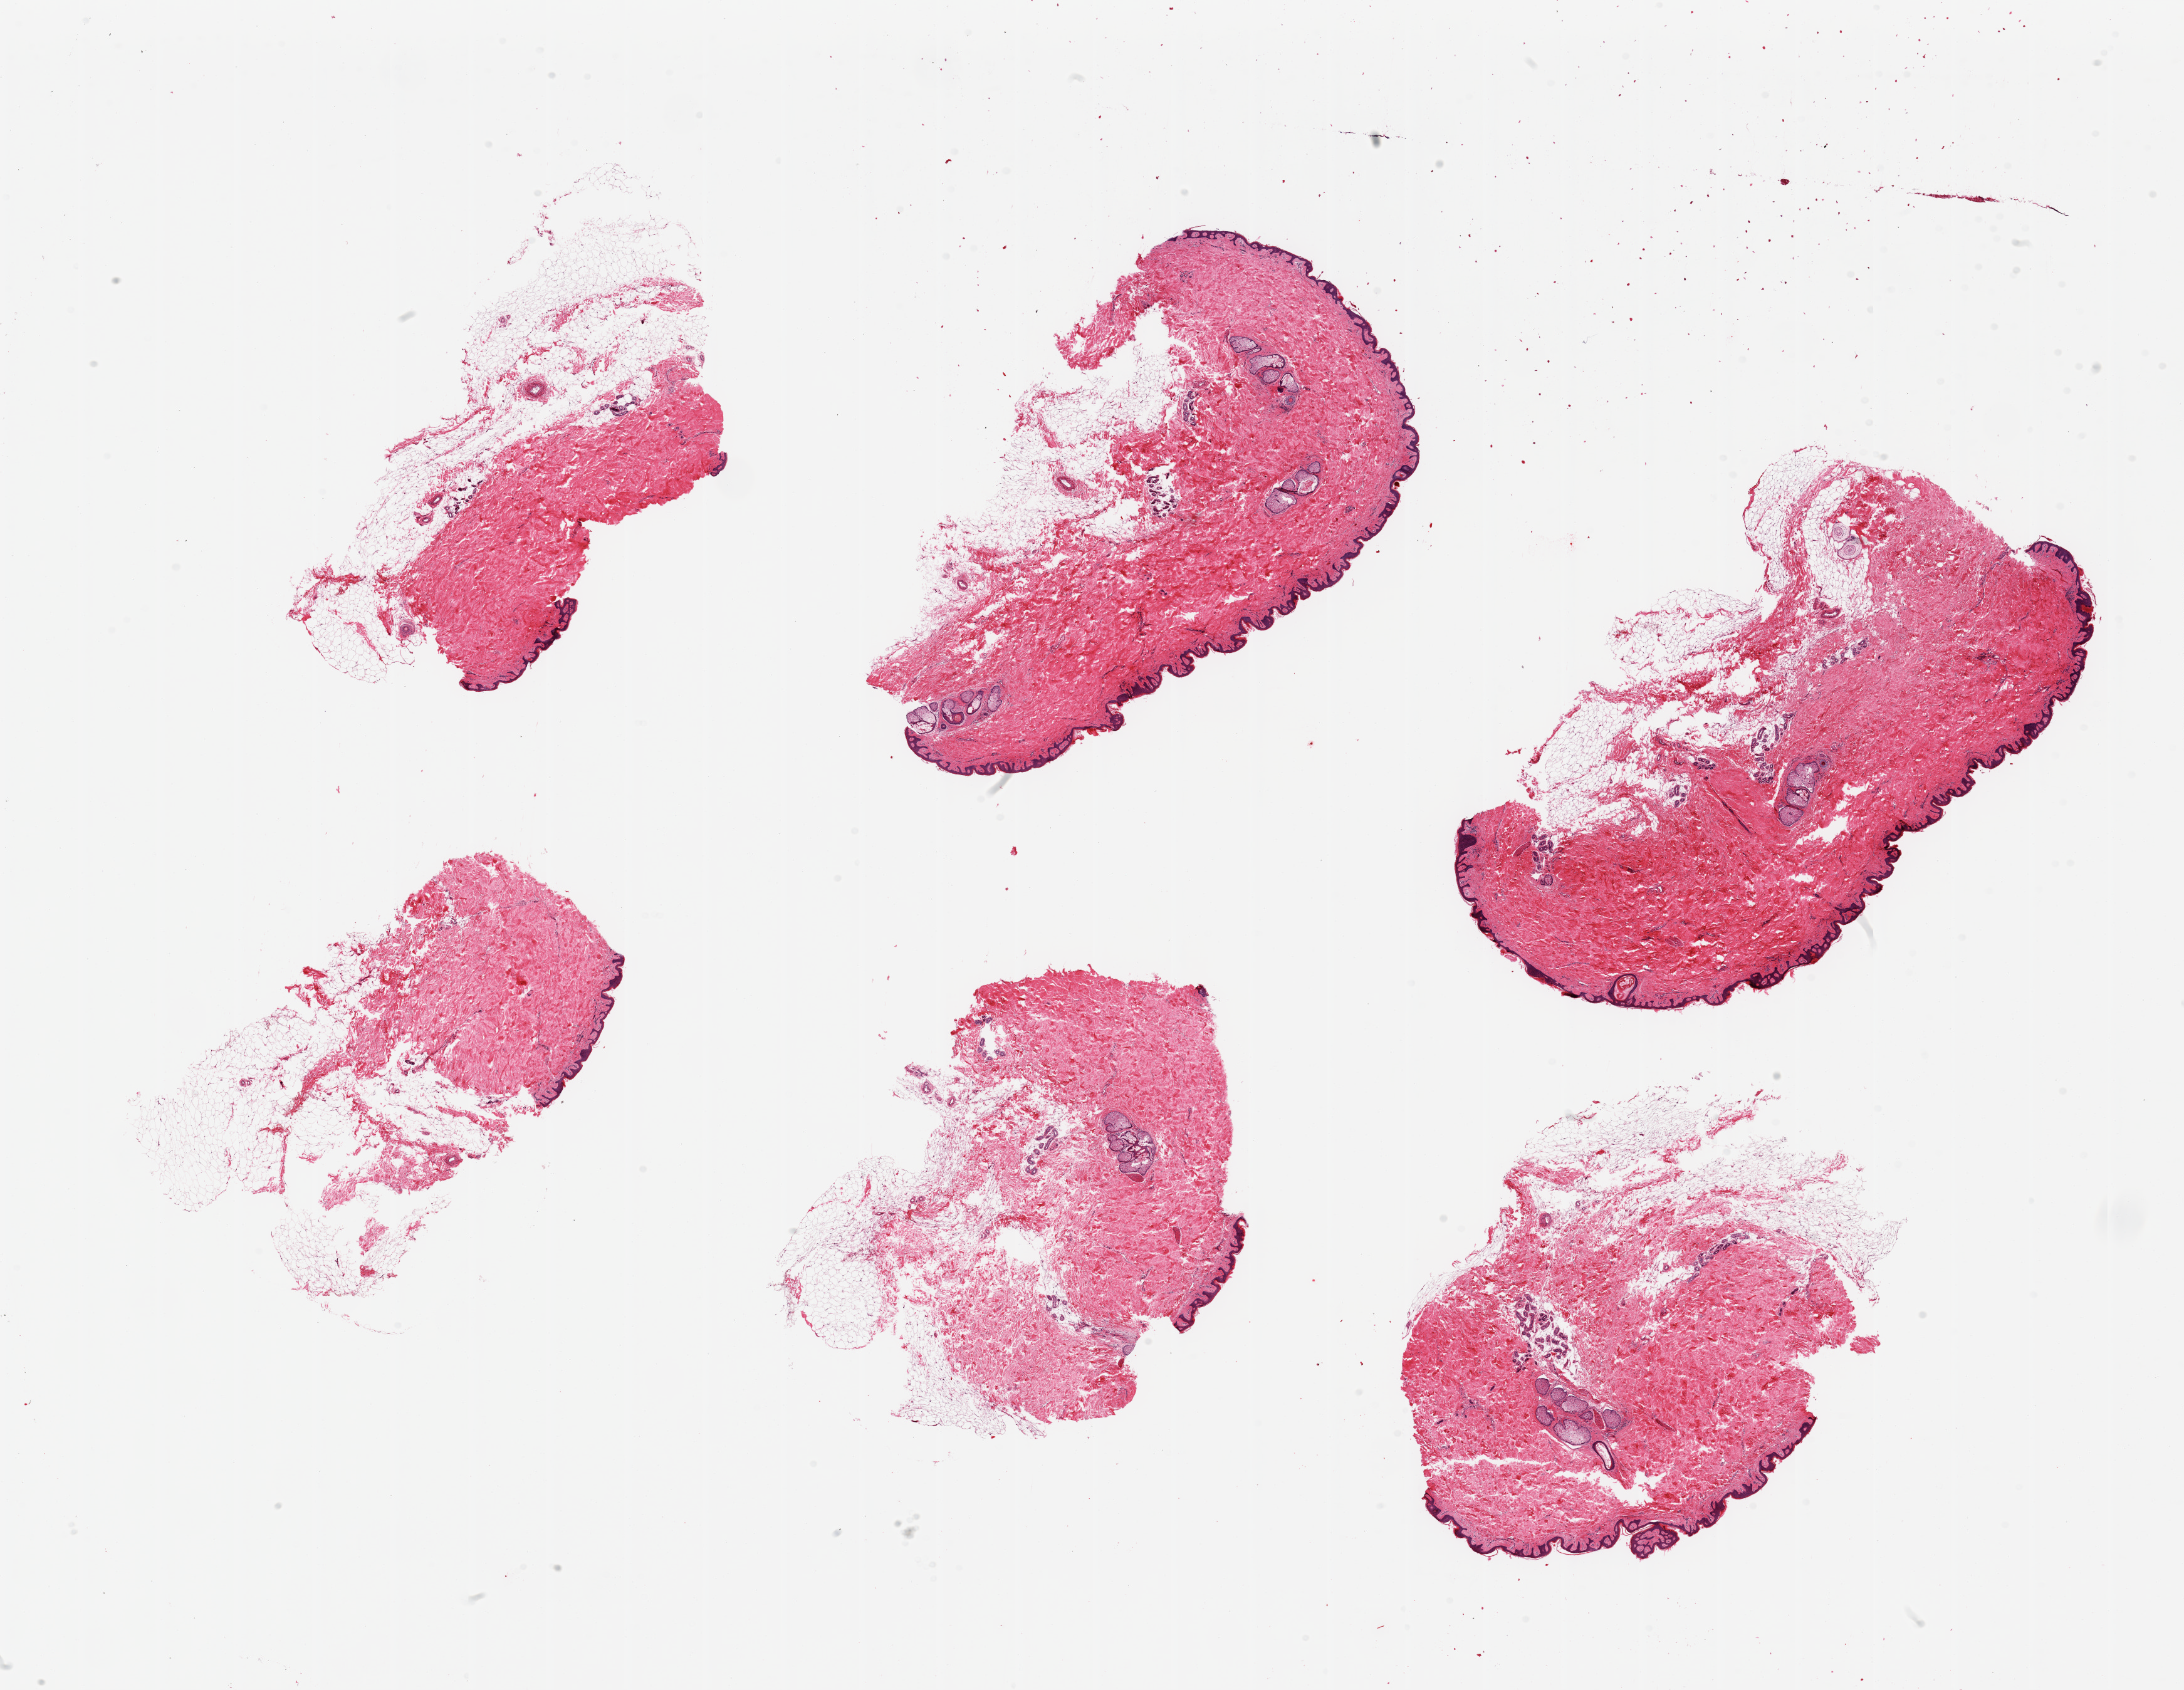
Whole-slide image, haematoxylin and eosin stain — low-resolution overview of the scanned area, about 27.6 x 21.3 mm, PAXgene-fixed paraffin-embedded (PFPE) section, sampled site (target tissue): skin of suprapubic region, donor tissue sample. Male donor.
Review note (as recorded): 6 pieces, moderate adherent dermal fat; squamous epithelium is ~40-50 microns.